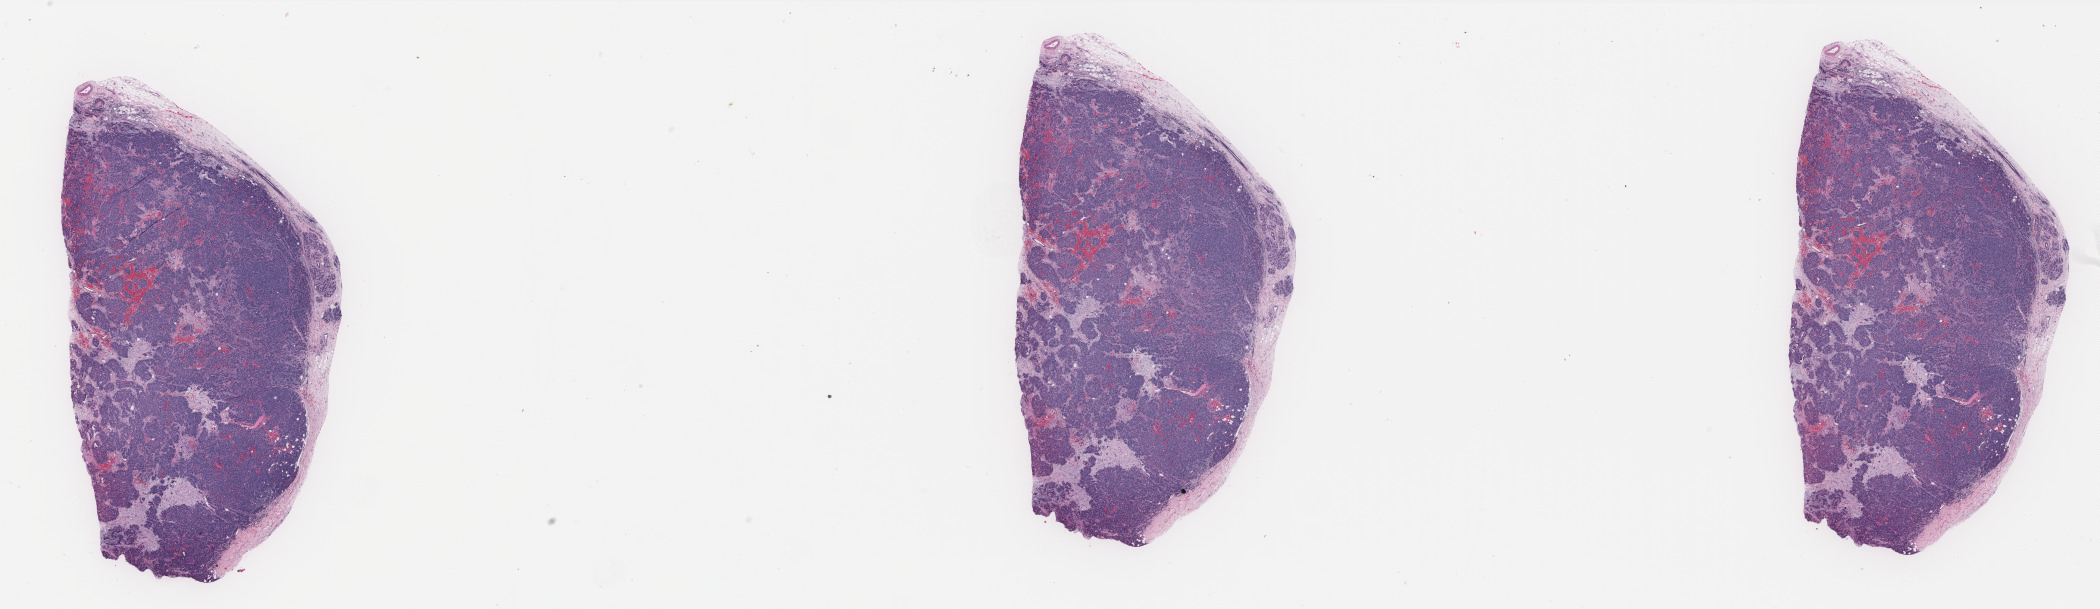
Hematoxylin and eosin (H&E) stained whole-slide image, whole scanned area (about 33.7 x 9.8 mm) shown as a low-resolution overview, FFPE section, sample: primary tumour, breast. Female, age 61 years at initial diagnosis.
Pathologic diagnosis: Infiltrating duct carcinoma, NOS. Lymph nodes positive (case pathology): 4 of 15 examined. AJCC pathologic stage: IIIA (6th edition).